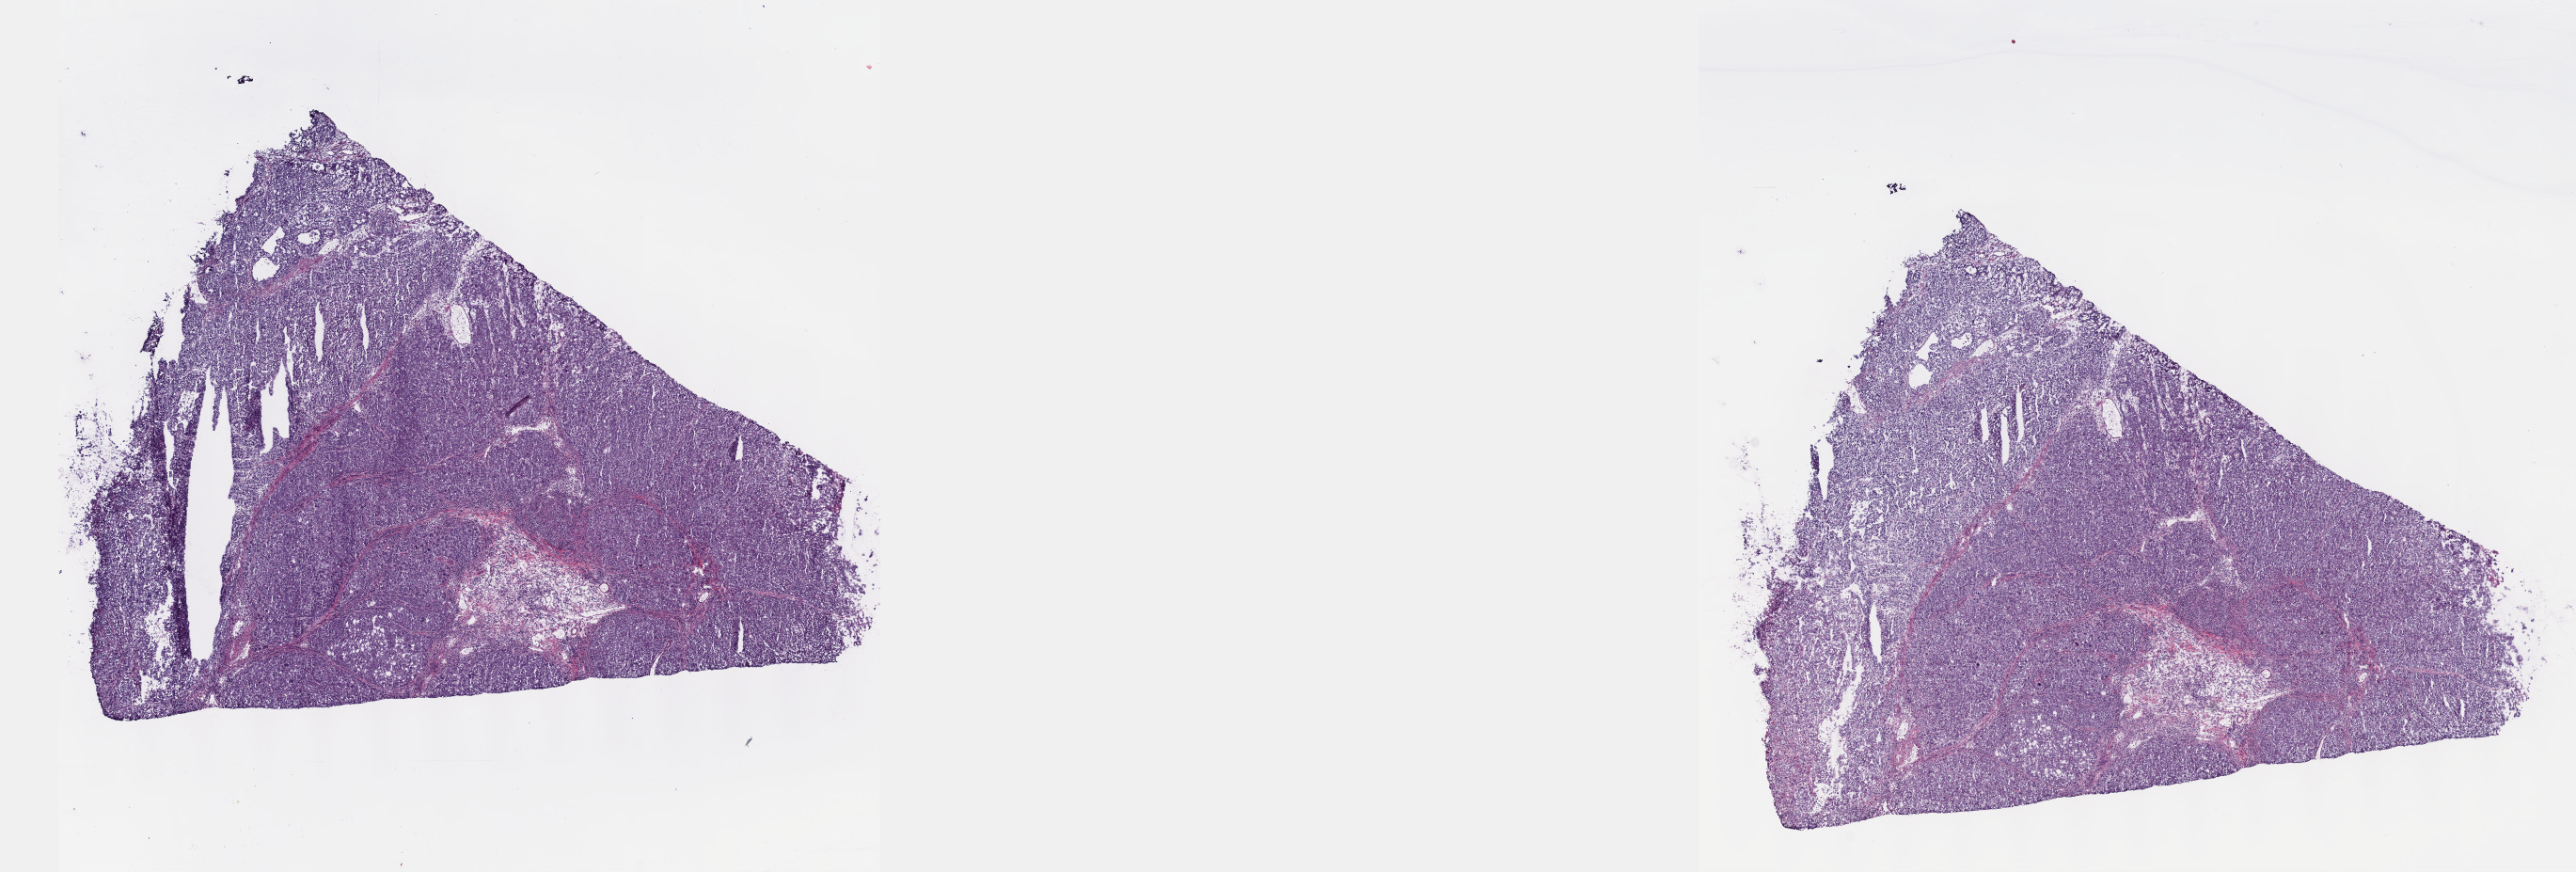
H&E-stained whole-slide image — a low-resolution overview of the entire scanned area, about 22.1 x 7.5 mm (acquisition: 40x scan). Frozen section from the top of the tissue portion. Sample: primary tumour, esophagus. Patient: male, age at initial diagnosis 81 years. Histologic grade: GX (grade cannot be assessed). Slide review estimates, as recorded: tumour cells 90%, tumour nuclei 95%, normal cells 0%, stromal cells 5%, necrosis 5%. Inflammatory infiltration, as recorded: lymphocyte infiltration 0%, monocyte infiltration 0%, neutrophil infiltration 0%.
* diagnosis: Adenocarcinoma, NOS (lower third of esophagus)
* AJCC pathologic stage: III (6th edition)